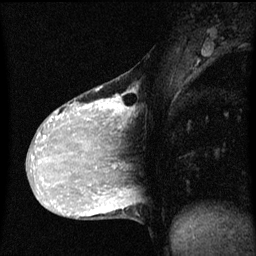
Breast MRI (dynamic contrast-enhanced), one sagittal slice. Slice 27 of 60 in the series (ordered by position). Dynamic contrast-enhanced series, image 2 of 3 at this slice position (ordered by acquisition). 1.5 T. TE 4.2 ms, TR 8 ms. 2 mm slice thickness. 256 × 256 image matrix, field of view 200 × 200 mm. Female patient, age 36 years.
Annotated regions visible in this slice (semi-automatic segmentation, software-assisted and operator-edited):
- analysis volume of interest (the breast-tissue region the enhancement analysis was run in; not a lesion): bounding box [x1, y1, x2, y2] px = [33, 72, 133, 169]
- tumour enhancement mask (voxels above the 70 % enhancement threshold inside the analysis volume of interest): [34, 86, 130, 169]